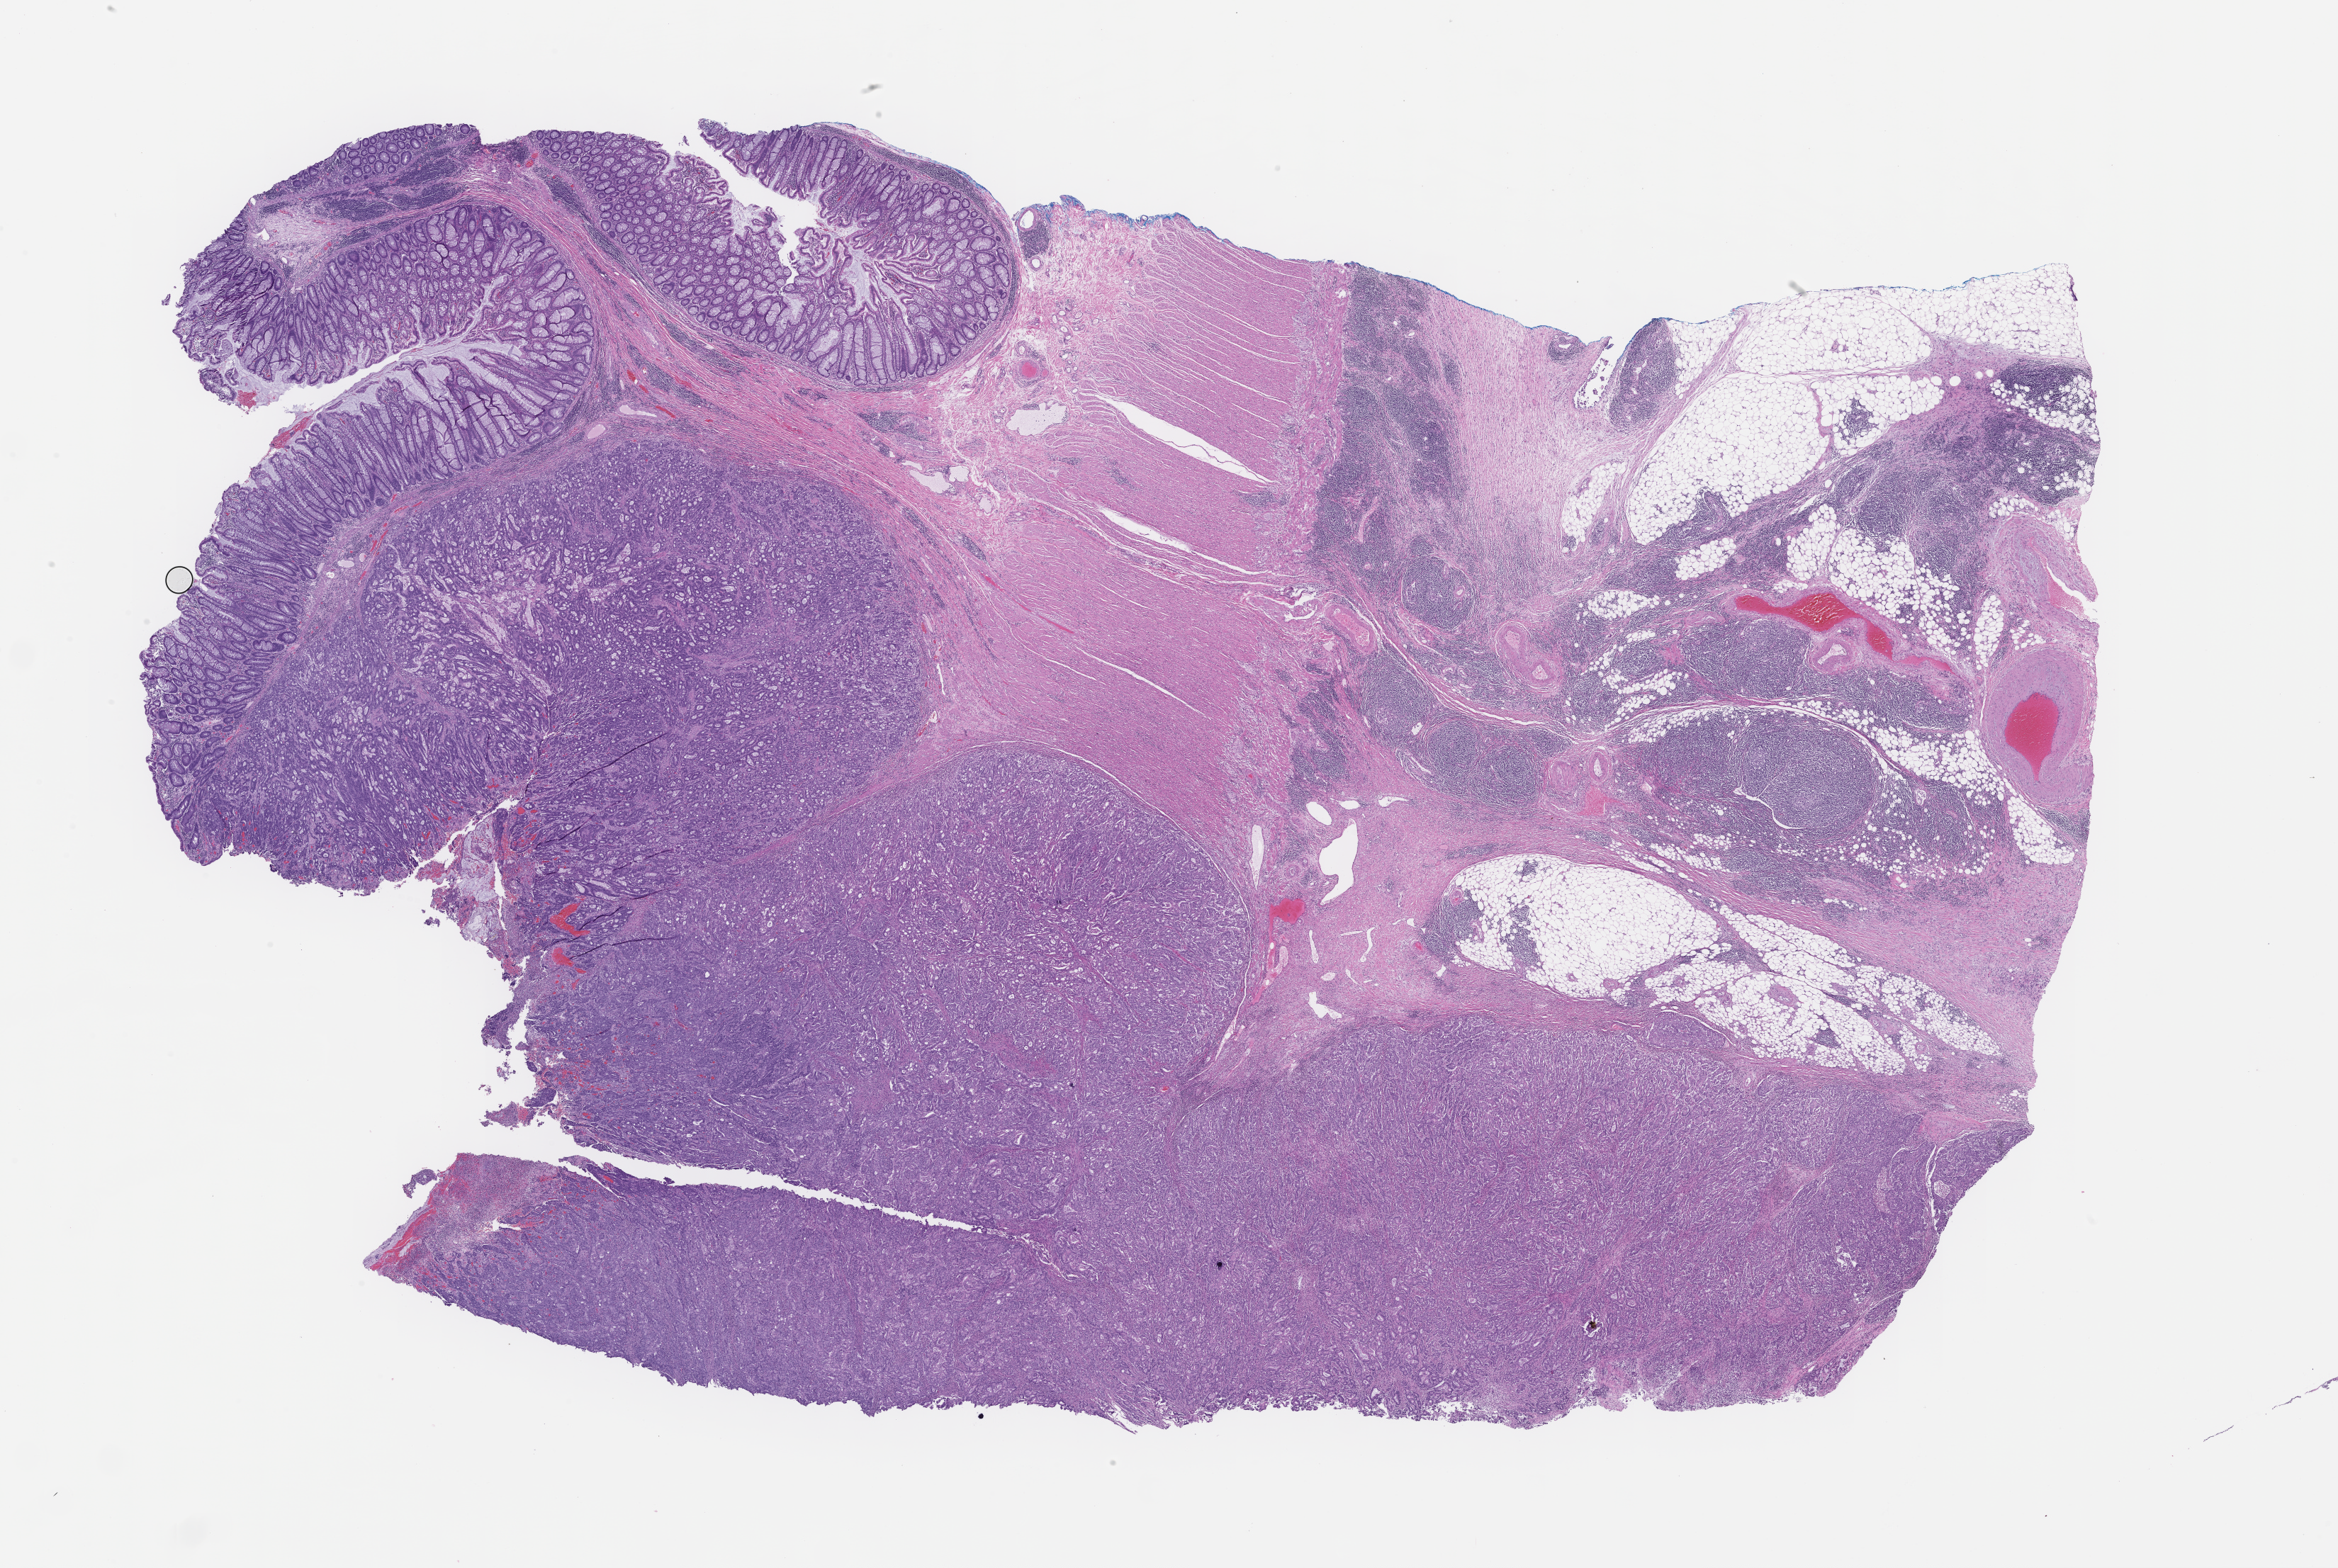
H&E whole-slide image, a low-resolution overview of the entire scanned area, about 26.6 x 17.9 mm. Formalin-fixed paraffin-embedded section. Site: colon. Specimen time point: archival tissue. Patient sex: female.
- this section: primary tumour tissue
- diagnosis: Colorectal Carcinoma